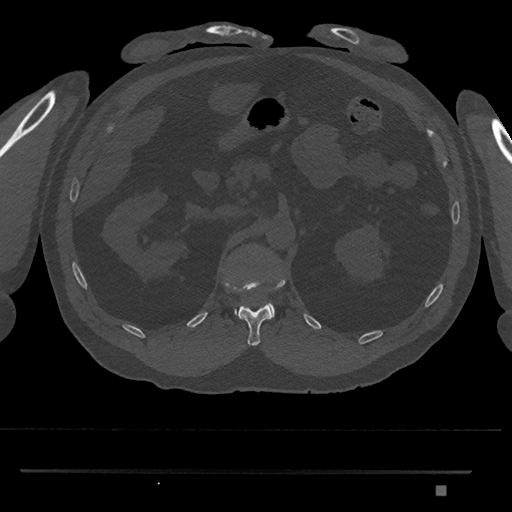
CT including the spine, one axial slice. Position 865 of 1134 along the scan axis. Bone window (W 1800 / L 400 HU). 0.5 mm slice thickness. 512 × 512 image matrix, field of view 429 × 429 mm. Male patient, age 65 years. Case-level facts recorded for this patient, not image findings: primary cancer: prostate.
Outlined on this slice (semi-automatically segmented with operator editing):
- L1 vertebra: bounding box [x1, y1, x2, y2] px = [234, 303, 275, 318]
- T12 vertebra: [223, 278, 286, 346]